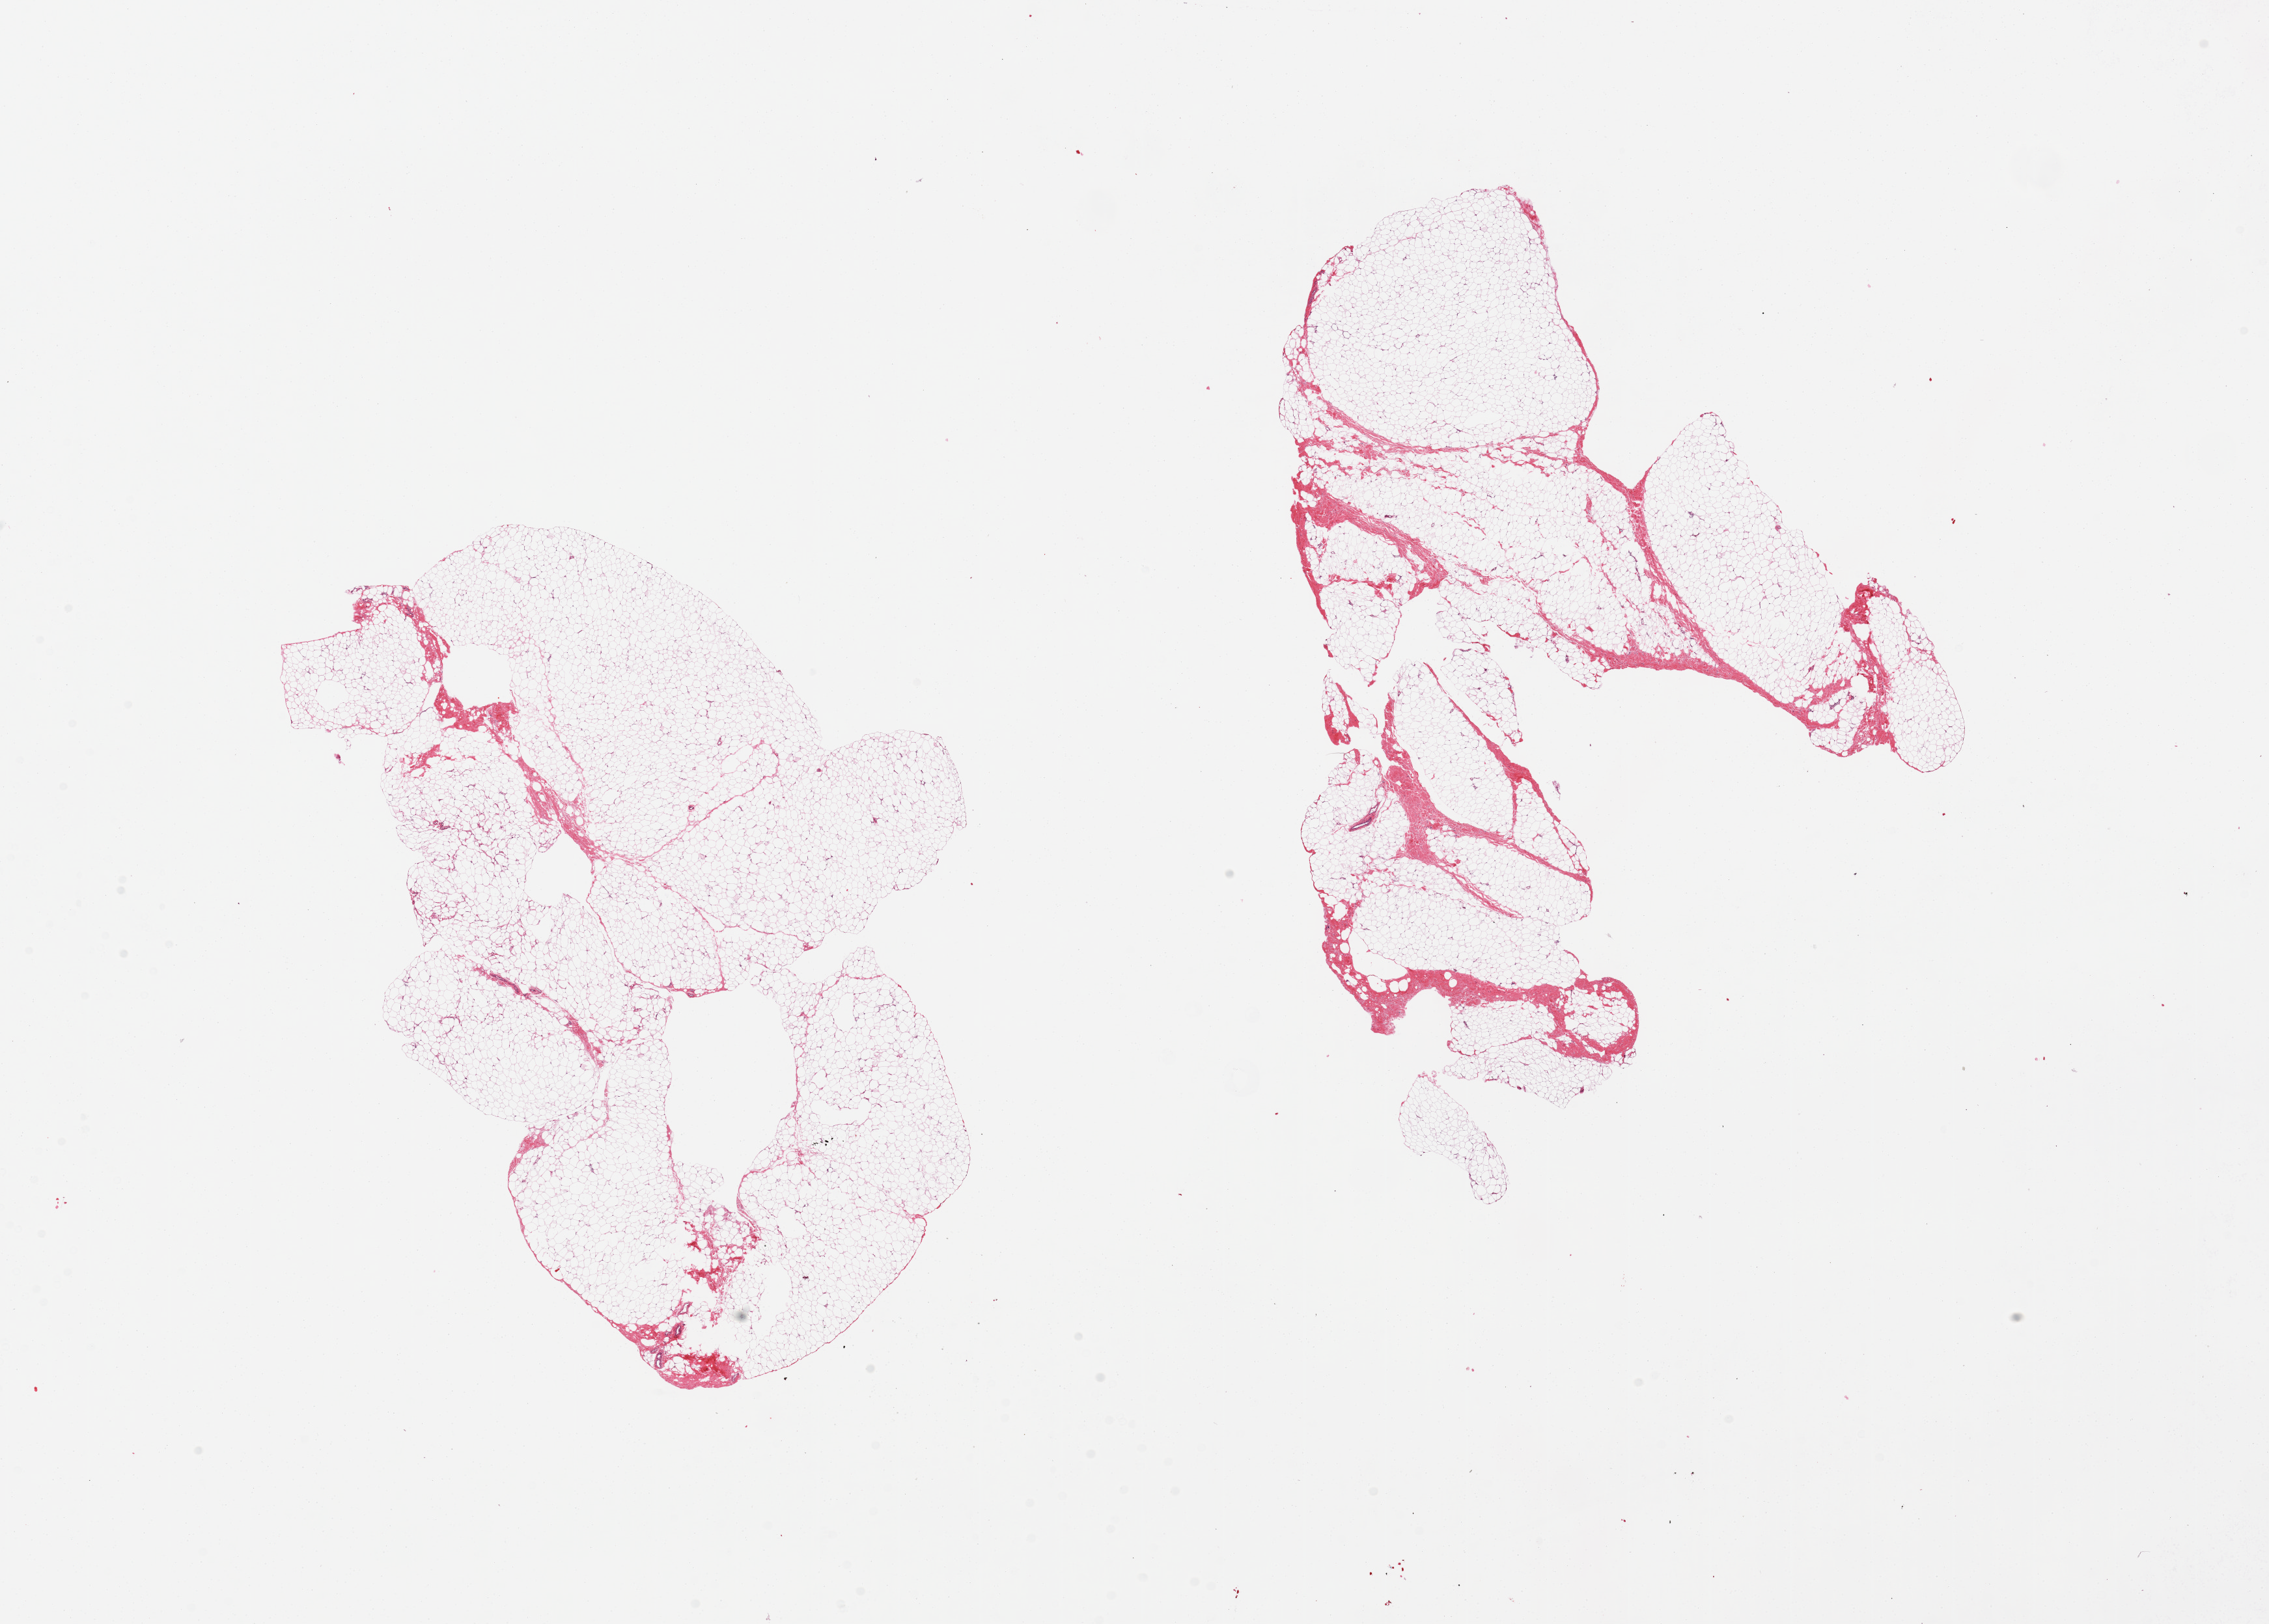
Hematoxylin and eosin (H&E) whole-slide image — shown as a low-resolution overview of the whole scanned area (about 27.6 x 19.7 mm). PAXgene-fixed paraffin-embedded (PFPE) section. Sampled site (target tissue): breast. Donor tissue sample.
Reviewer comment on this tissue sample: 2 pieces, fibroadipose tisue; no ductal elements noted.